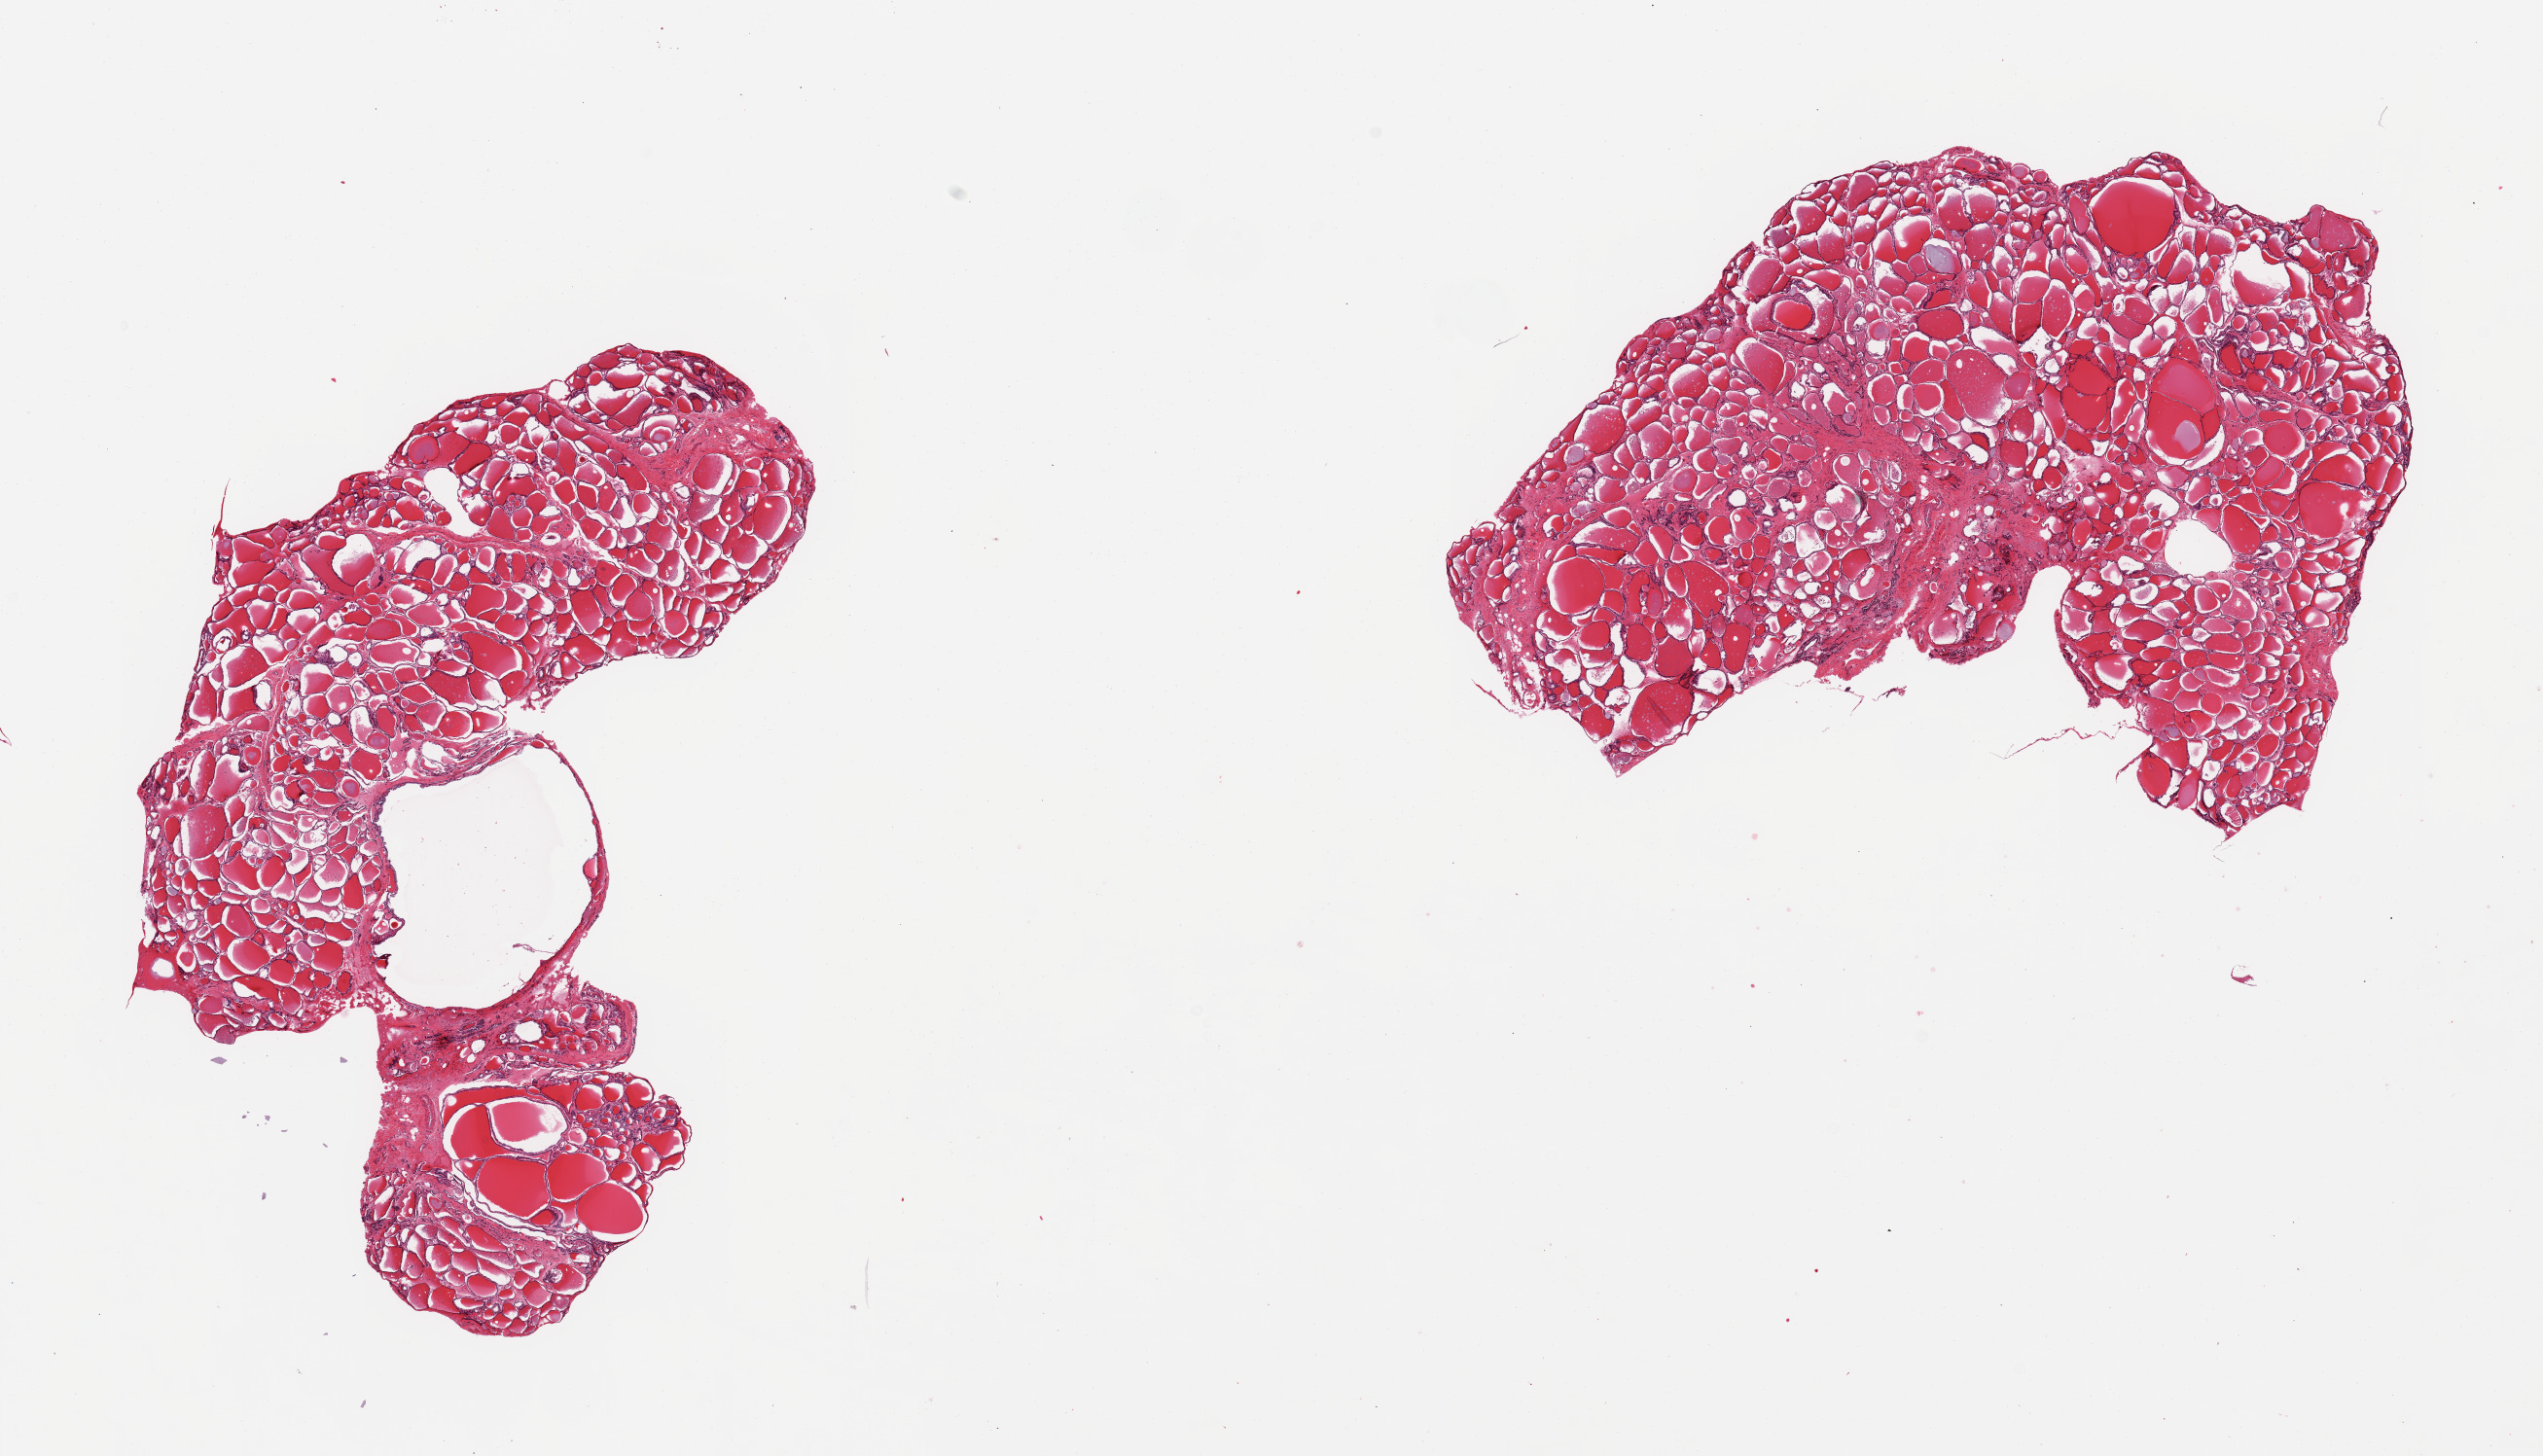
Digitized H&E-stained section, shown as a low-resolution overview of the whole scanned area (about 20.7 x 11.8 mm, slide scanned at 20x), PAXgene-fixed paraffin-embedded (PFPE) section, target tissue: thyroid, tissue donor sample. Male donor.
Review note (as recorded): 2 pieces; nodular hyperplasia.